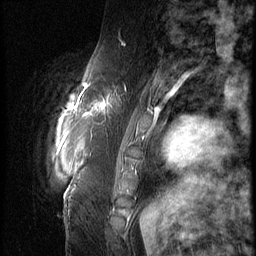
Breast MRI (dynamic contrast-enhanced), one sagittal slice; position 15 of 66 along the scan axis; 3 images stored at this slice position (order not interpretable as contrast timing); 1.5 T; TE 4.2 ms, TR 9 ms; 2.5 mm slice thickness; 256 × 256 image matrix, field of view 180 × 180 mm. Female patient, age 57 years. From the clinical record (not read from this slice): setting: breast cancer imaged before/during neoadjuvant chemotherapy; receptor status: triple-negative.
Annotated regions visible in this slice (semi-automatically segmented with operator editing):
- analysis volume of interest (the breast-tissue region the enhancement analysis was run in; not a lesion): box from (x=86, y=74) to (x=138, y=129) px
- tumour enhancement mask (voxels above the 140 % enhancement threshold inside the analysis volume of interest): (x=86, y=85)–(x=111, y=117)